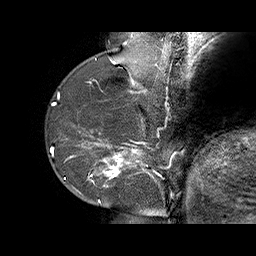
Breast MRI (dynamic contrast-enhanced), one sagittal slice. Slice 18 of 70 in the series (ordered by position). Dynamic contrast-enhanced series, time point 2 of 6 at this slice position (early post-contrast). 1.5 T. TE 4.5 ms, TR 32.4 ms. 3 mm slice thickness. 256 × 256 image matrix, field of view 180 × 180 mm. Female patient. Case-level facts recorded for this patient, not image findings: setting: breast cancer imaged before/during neoadjuvant chemotherapy; receptor status: HR-positive, HER2-negative.
Annotated regions visible in this slice (semi-automatically segmented with operator editing):
- analysis volume of interest (the breast-tissue region the enhancement analysis was run in; not a lesion): bounding box <71,128,159,202> (left, top, right, bottom; pixels)
- tumour enhancement mask (voxels above the 100 % enhancement threshold inside the analysis volume of interest): <71,129,155,202>